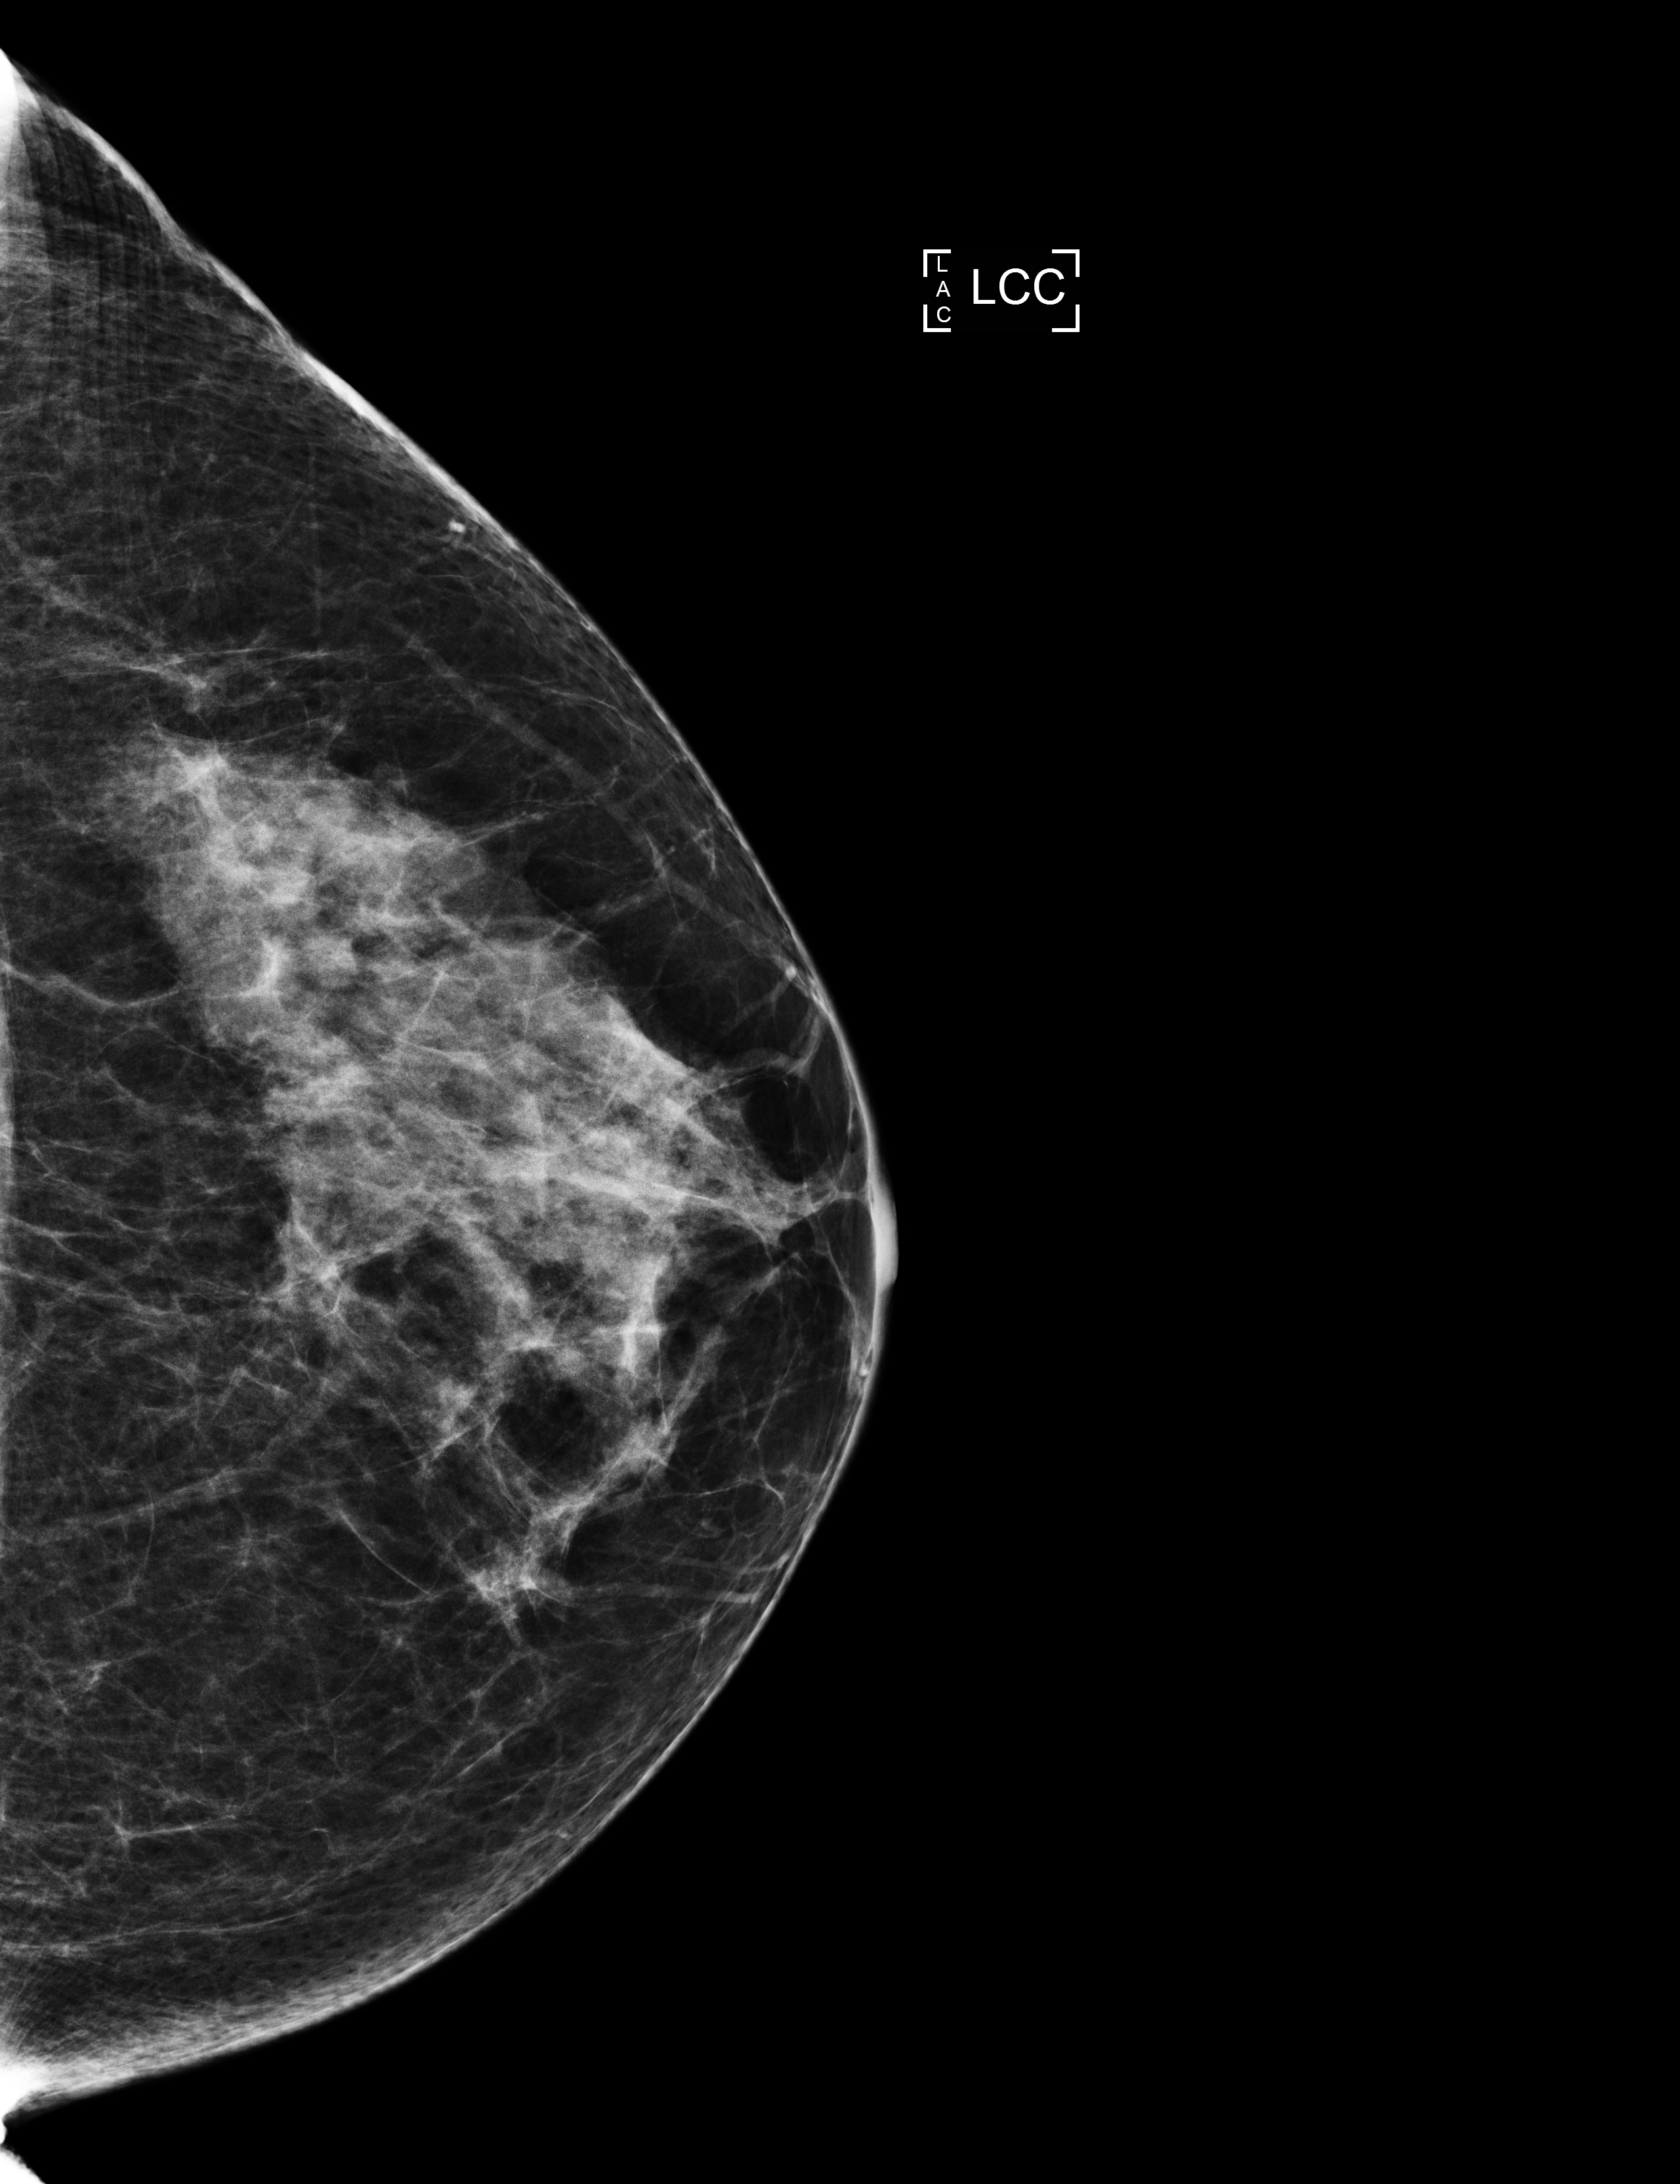
Annual screening mammography examination. Female patient, age 63 years.
Image type: full-field digital mammogram. Breast: left. Projection: cranio-caudal projection.